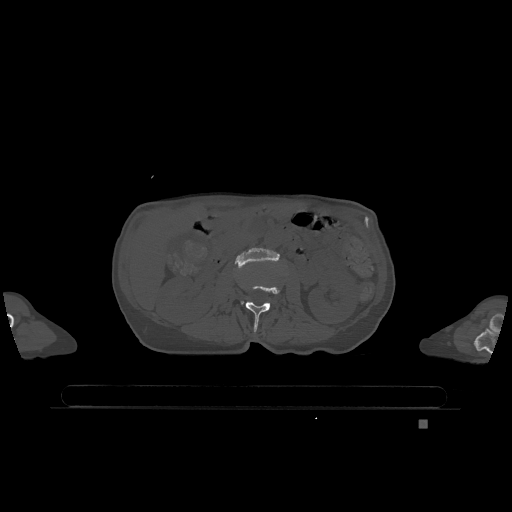
CT including the spine, one axial slice. Slice 399 of 1317 in the series (ordered by position). Bone window (W 1800 / L 400 HU). 512 × 512 image matrix. Female patient, age 74 years. Case-level facts recorded for this patient, not image findings: primary cancer: lung; vertebrae with lytic lesions (as recorded): T1, T4, T5, T6, L4, L5.
Outlined on this slice (semi-automatically segmented with operator editing):
- L2 vertebra: box from (x=246, y=286) to (x=280, y=332) px
- L3 vertebra: (x=235, y=248)–(x=279, y=304)